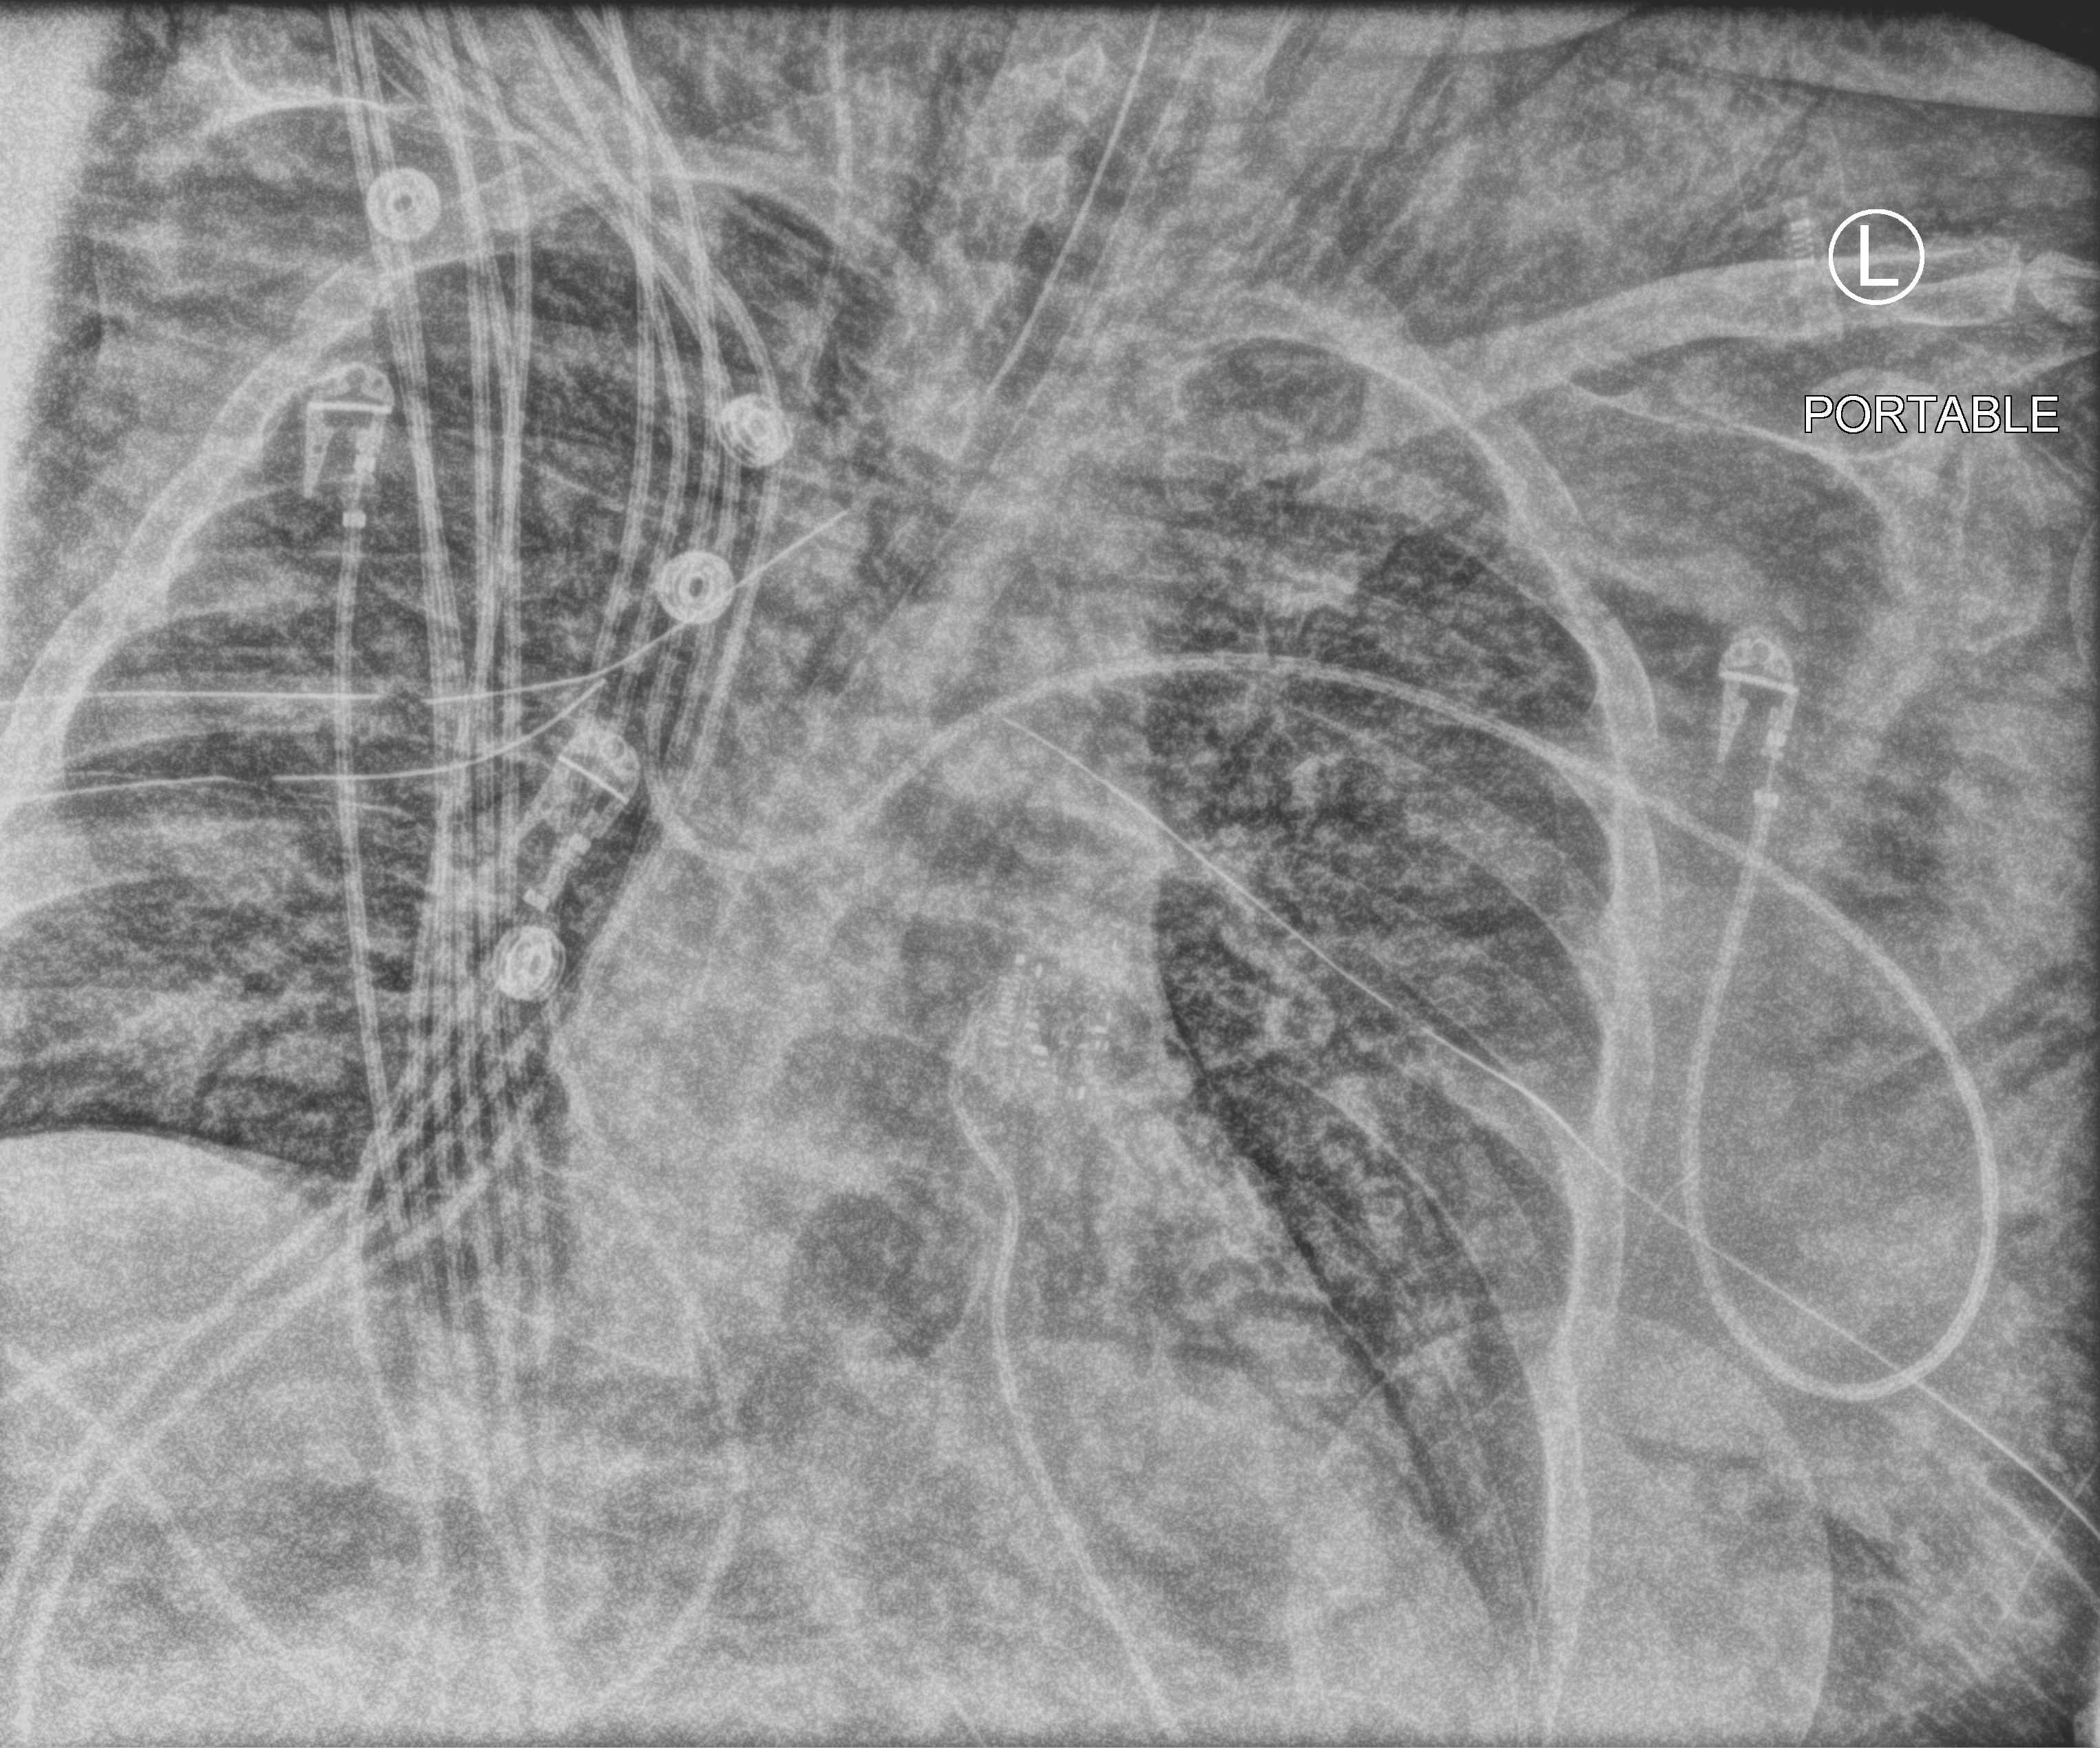
Chest X-ray (portable), anteroposterior (AP) projection. Adult patient hospitalised with COVID-19, age 18–59 years.
Hospital-stay facts (about this admission, not read from this image; timing relative to this image not recorded):
- length of hospital stay: 26 days
- mechanically ventilated during this hospital stay: yes